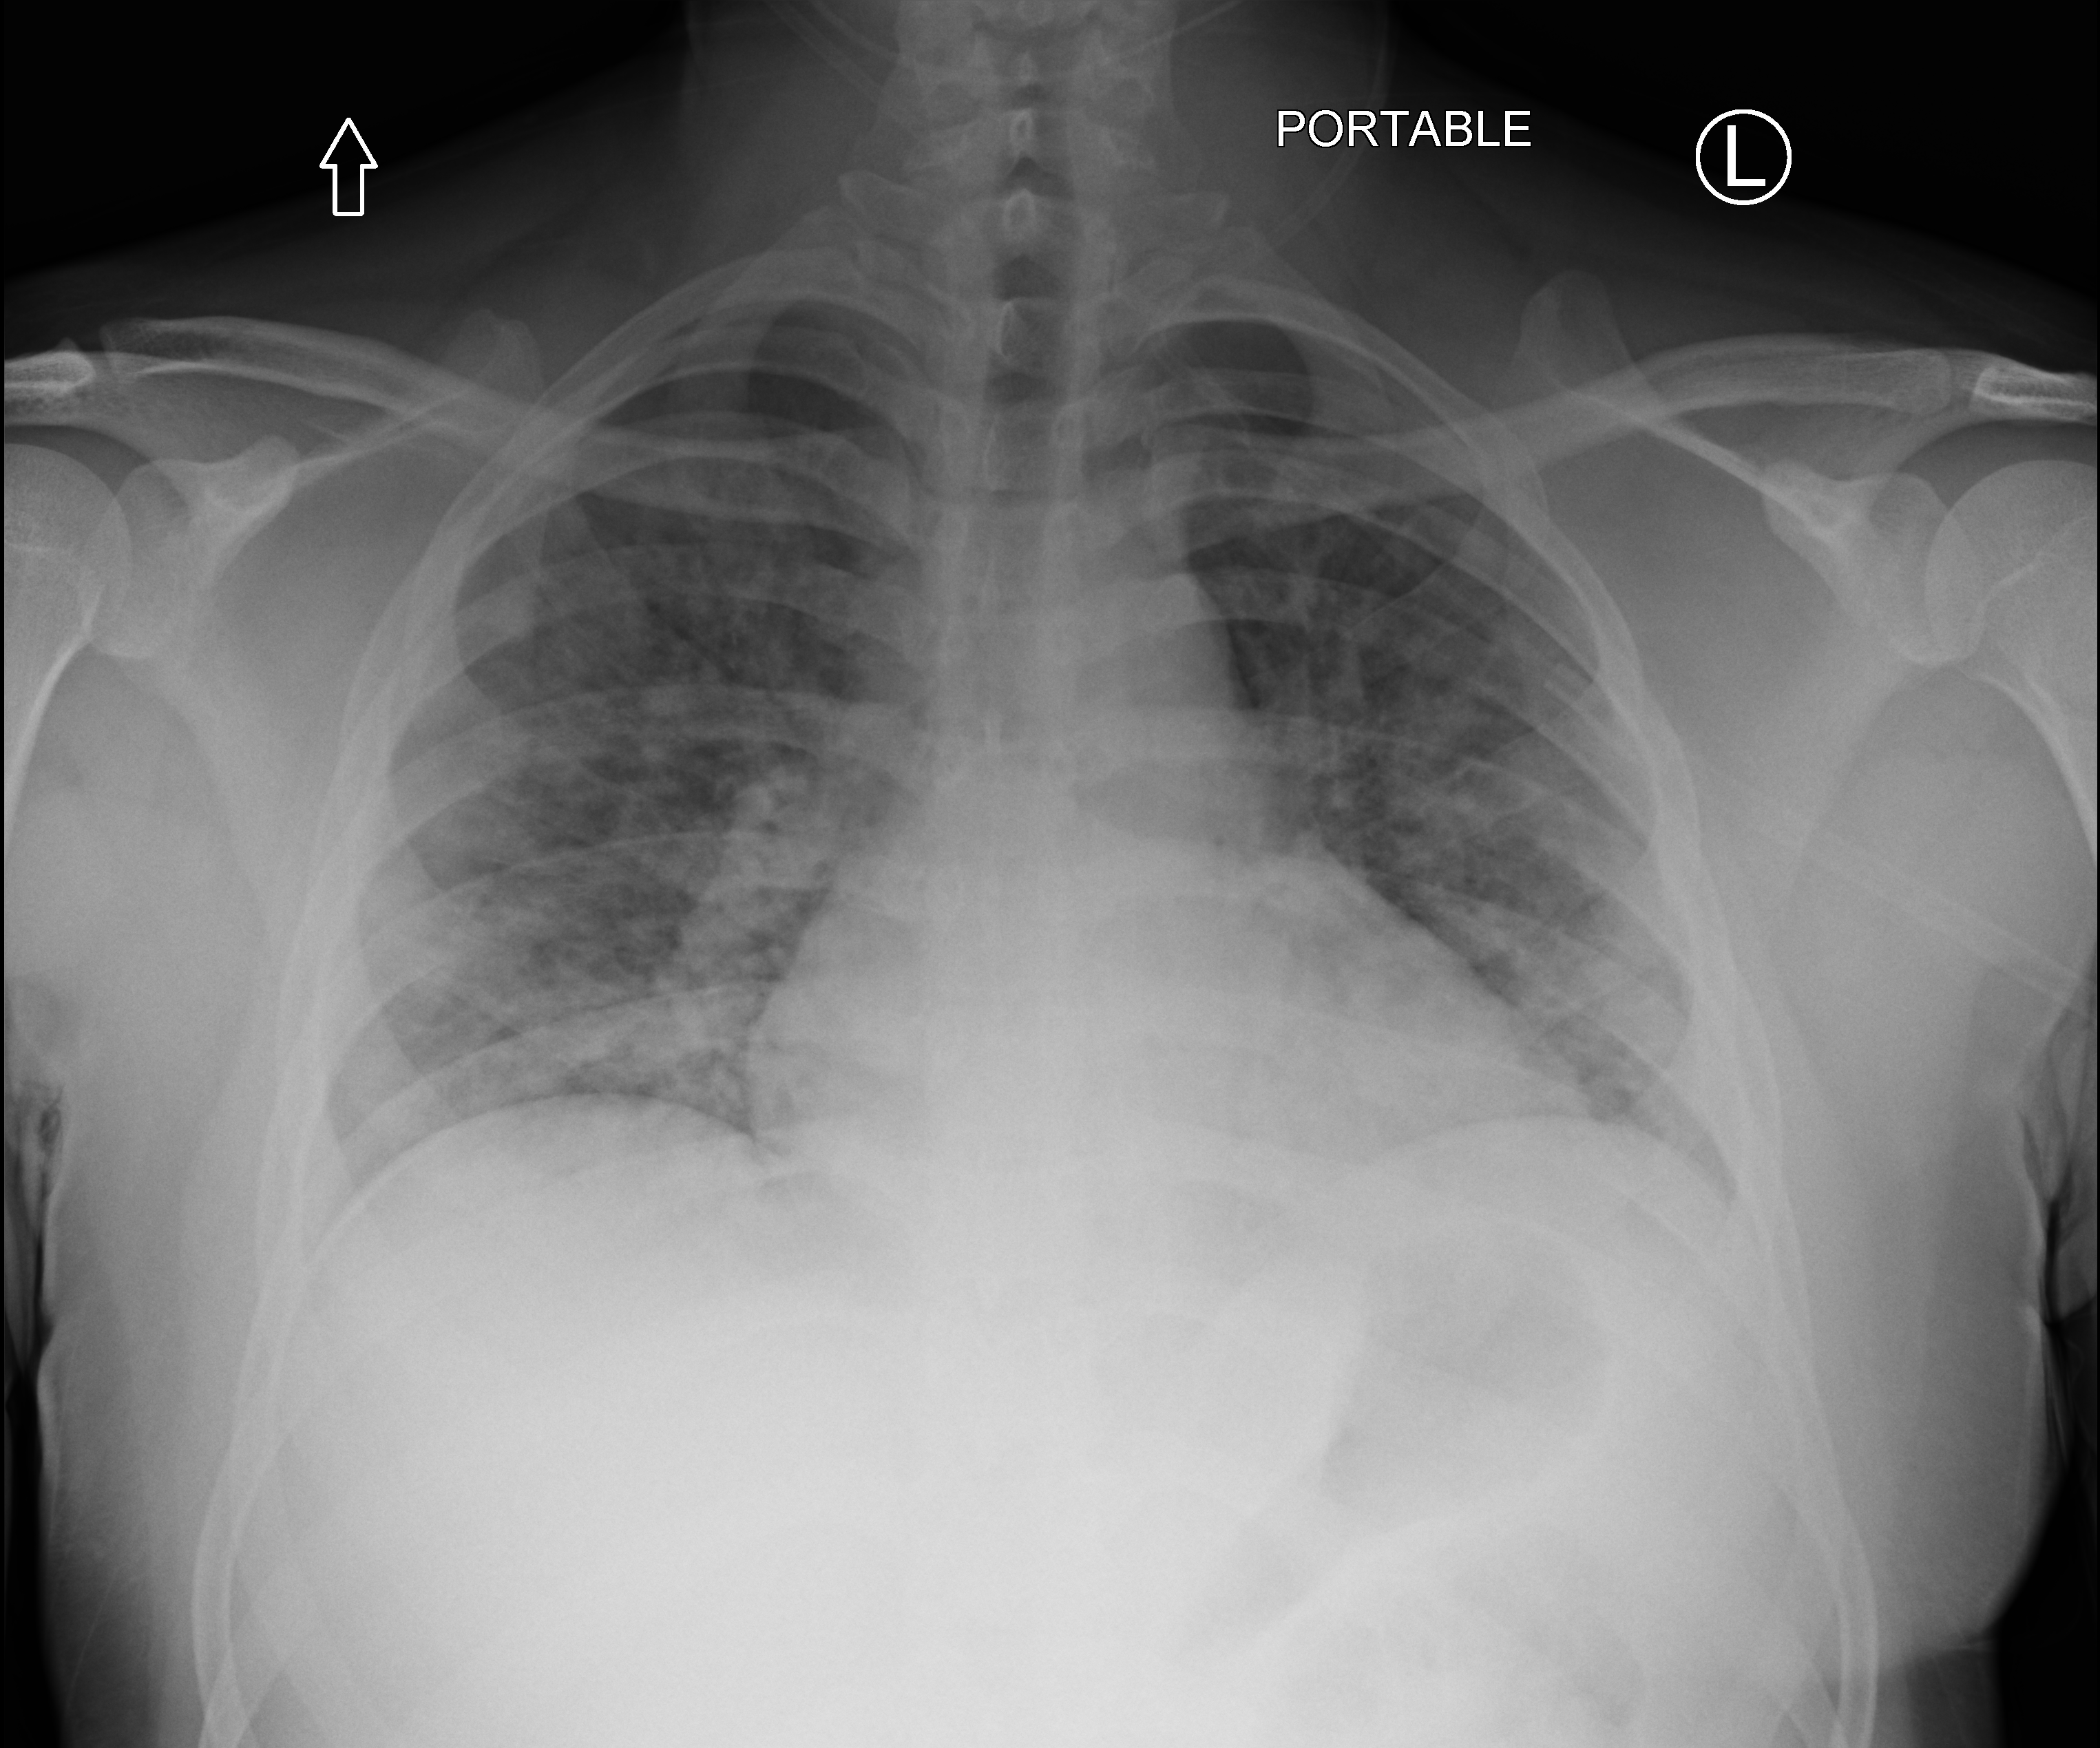
Chest X-ray (portable), anteroposterior (AP) projection. Patient hospitalised with COVID-19; male, aged 18–59 years.
From the hospital-stay record, not from the radiograph (when in the stay this image was taken is not recorded):
- admitted to intensive care during this hospital stay: no
- mechanically ventilated during this hospital stay: yes